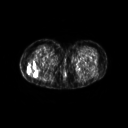
FDG PET of an extremity soft-tissue mass (from a PET/CT study), one axial slice; position 26 of 267 along the scan axis; 3.27 mm slice thickness; 128 × 128 image matrix, field of view 600 × 600 mm. Female patient, age 57 years. From the clinical record (not read from this slice): histological type: epithelioid sarcoma with vascular differentiation; site of the primary tumour: right buttock.
Outlined on this slice (expert contour drawn on MRI and transferred to this co-registered scan by the dataset authors):
- gross tumour volume (mass): bounding box <27,60,37,75> (left, top, right, bottom; pixels)